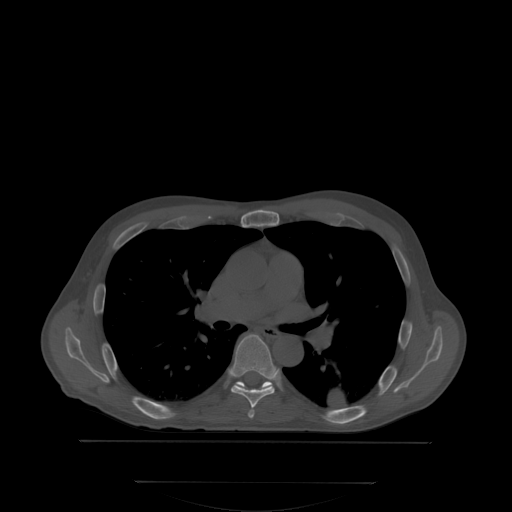
CT including the spine, one axial slice. Position 235 of 350 along the scan axis. Bone window (W 1800 / L 400 HU). 2.5 mm slice thickness. 512 × 512 image matrix. Patient: male, 58 years. From the clinical record (not read from this slice): primary cancer: prostate; vertebrae with lytic lesions (as recorded): L1.
Structures marked on this image (semi-automatic segmentation, software-assisted and operator-edited):
- T6 vertebra: bounding box [x1, y1, x2, y2] px = [230, 335, 276, 417]
- T7 vertebra: [234, 381, 272, 391]